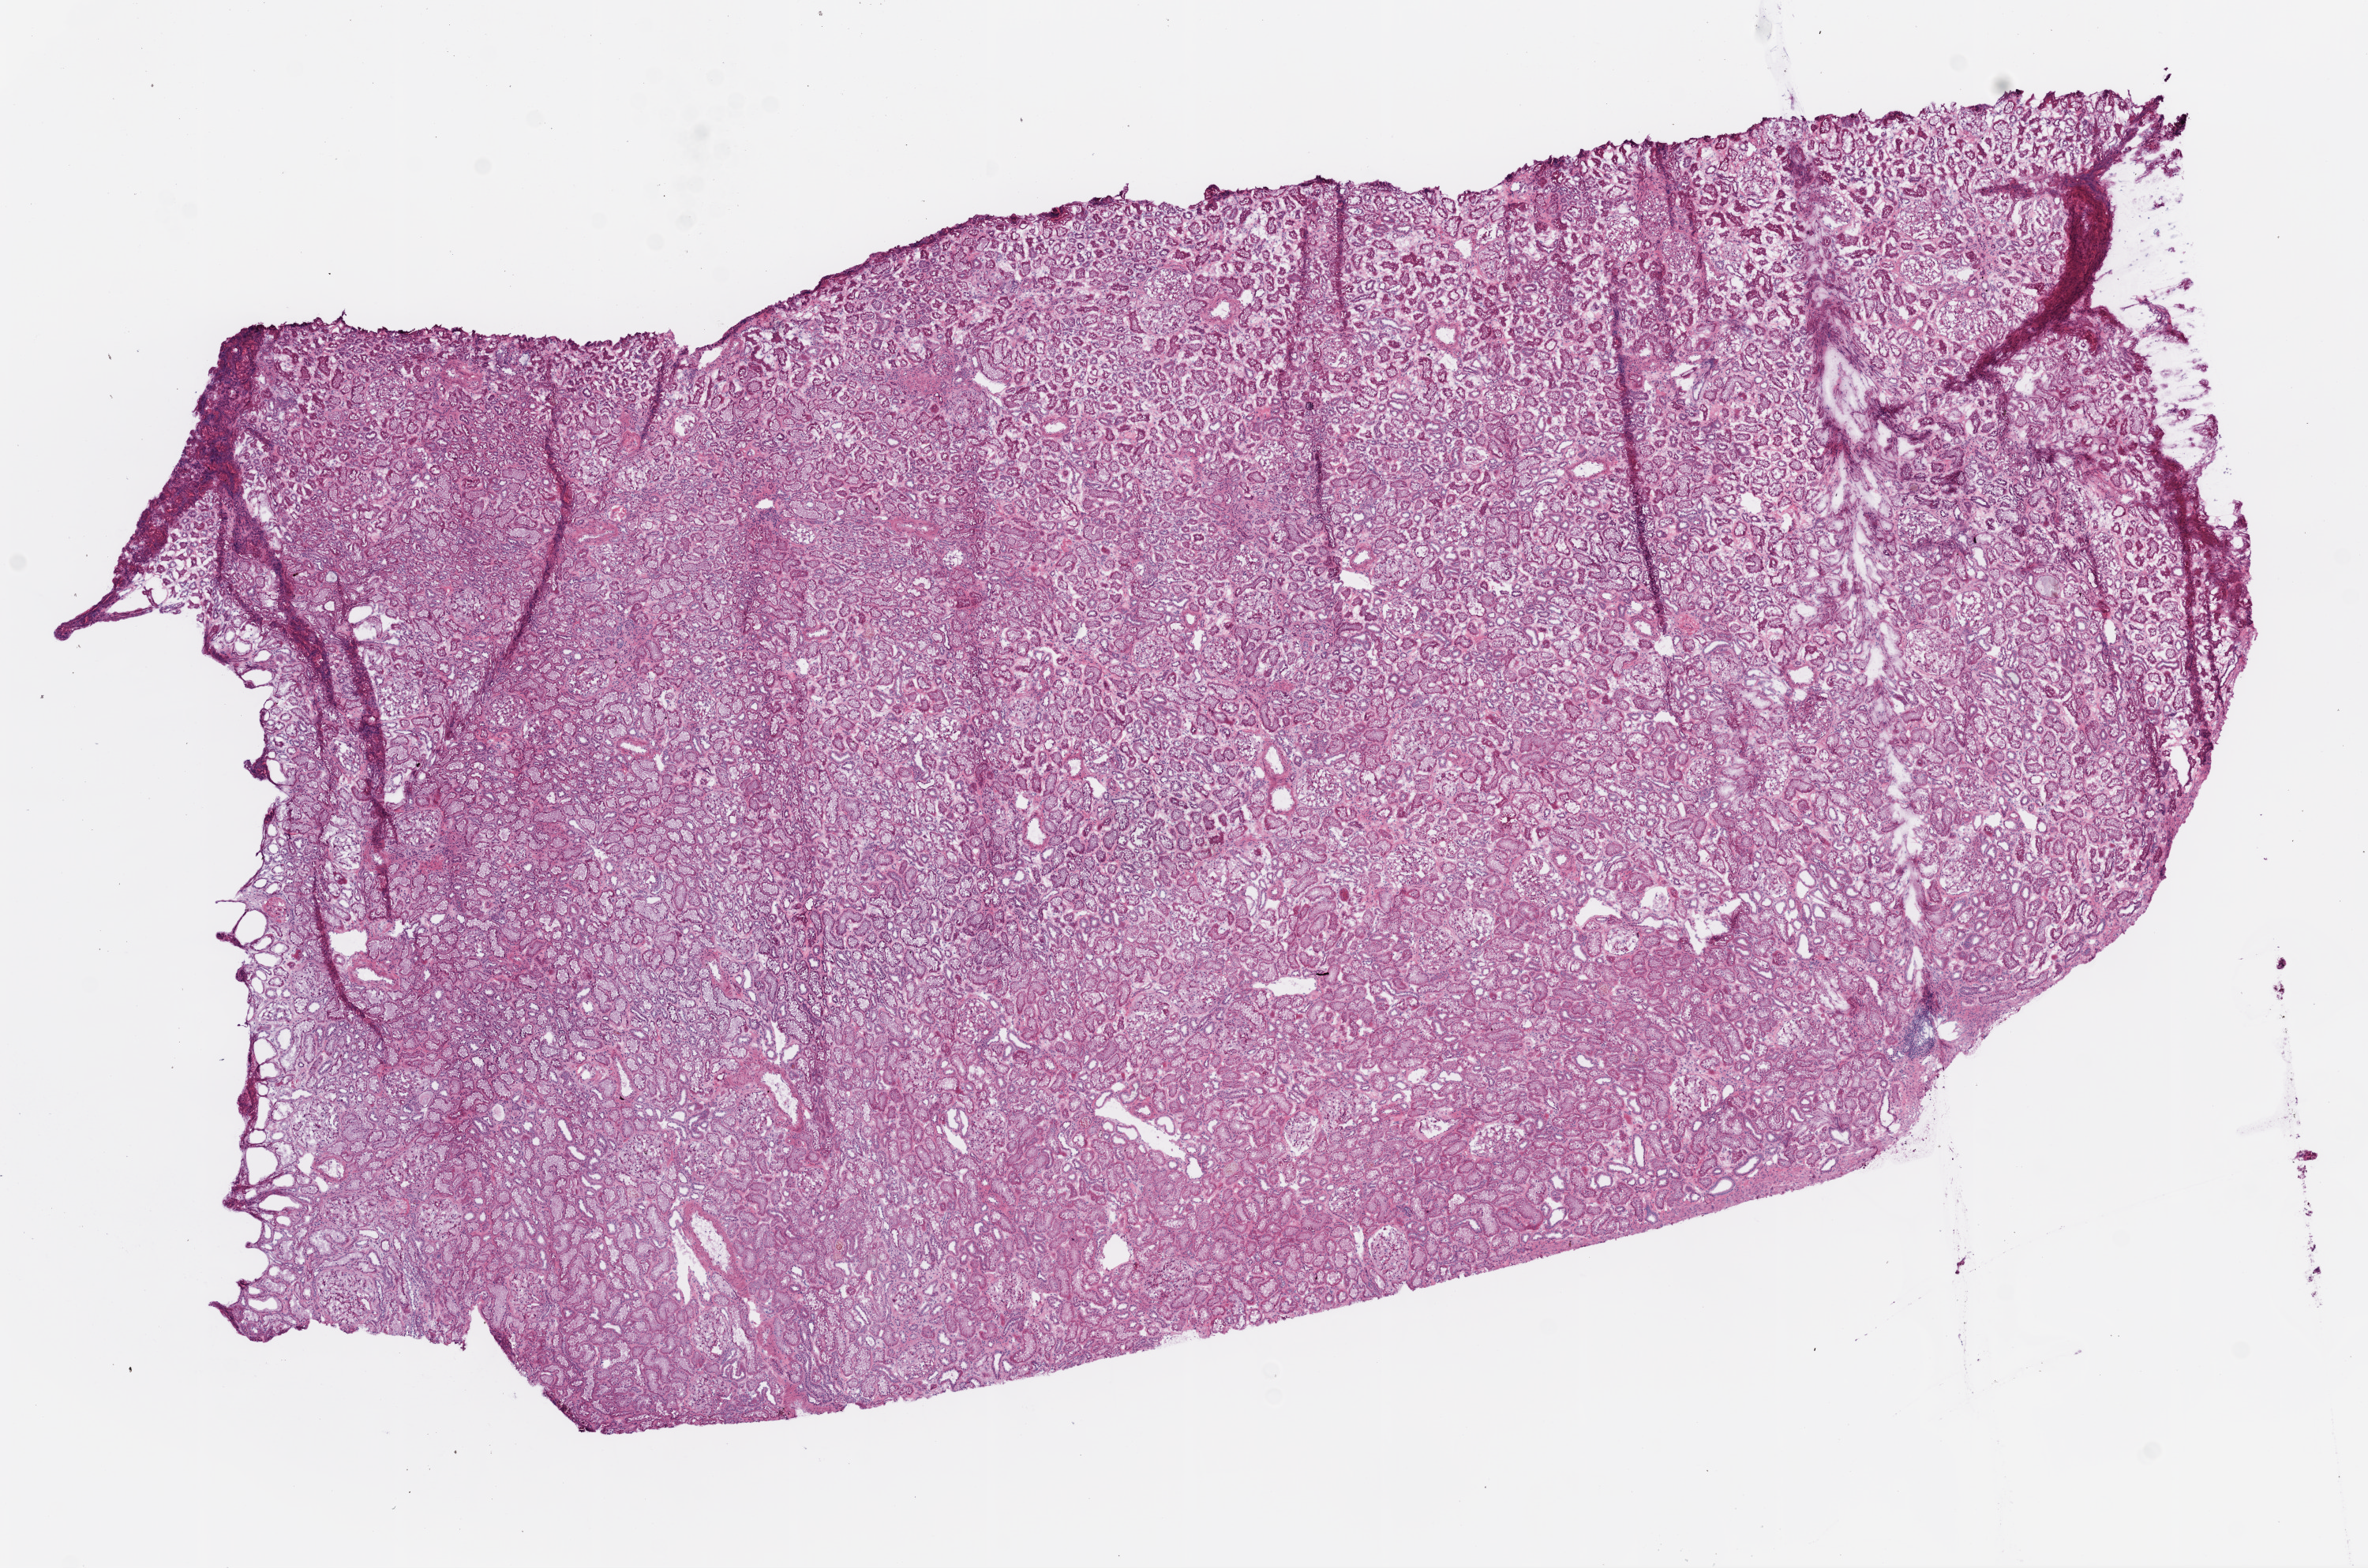
Digitized H&E tissue section (whole slide), a low-resolution overview of the entire scanned area, about 12.0 x 8.0 mm (acquisition: 20x scan); frozen section from the top of the tissue portion; solid tissue normal (non-tumour tissue) sample from the kidney. Patient: male, age at initial diagnosis 53 years.
This section: solid tissue normal sample (biorepository sample class). Patient diagnosis: Clear cell adenocarcinoma, NOS.